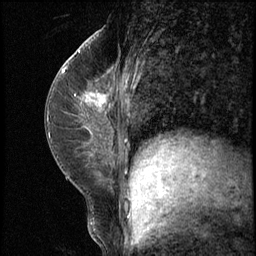
Breast MRI (dynamic contrast-enhanced), one sagittal slice; position 29 of 62 along the scan axis; 3 images stored at this slice position (order not interpretable as contrast timing); 1.5 T; TE 4.2 ms, TR 8.7 ms; 256 × 256 image matrix, field of view 180 × 180 mm. Patient: female, 35 years. From the clinical record (not read from this slice): setting: breast cancer imaged before/during neoadjuvant chemotherapy; receptor status: HER2-positive.
Structures marked on this image (semi-automatic segmentation, software-assisted and operator-edited):
- analysis volume of interest (the breast-tissue region the enhancement analysis was run in; not a lesion): bounding box (x1, y1, x2, y2) in pixels: (71, 78, 120, 139)
- tumour enhancement mask (voxels above the 140 % enhancement threshold inside the analysis volume of interest): (91, 94, 105, 106)